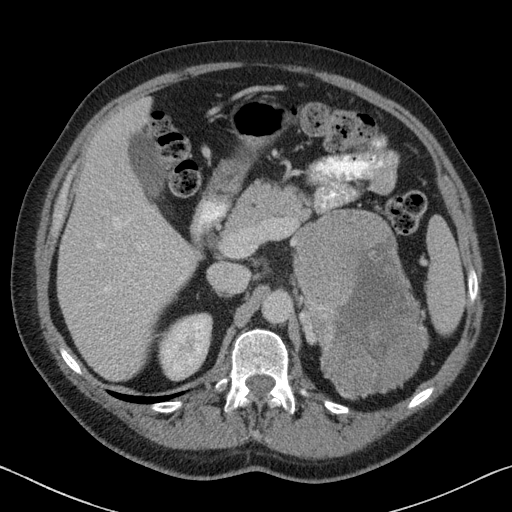
Contrast-enhanced abdominal CT, one axial slice. Slice 49 of 88 in the series (ordered by position). Reconstruction kernel B31f. 120 kVp. Intravenous contrast given. Soft-tissue window (W 400 / L 40 HU). 3 mm slice thickness. 512 × 512 image matrix, field of view 366 × 366 mm. Male patient, age 51 years. From the clinical record (not read from this slice): diagnosis: adrenocortical carcinoma; tumour side: left adrenal; tumour size at pathology: 16.5 cm; Ki-67 index: 30 %; stage (as recorded): 2.
Annotated regions visible in this slice (semi-automatically segmented with operator editing):
- mass: bounding box (x1, y1, x2, y2) in pixels: (299, 210, 424, 397)